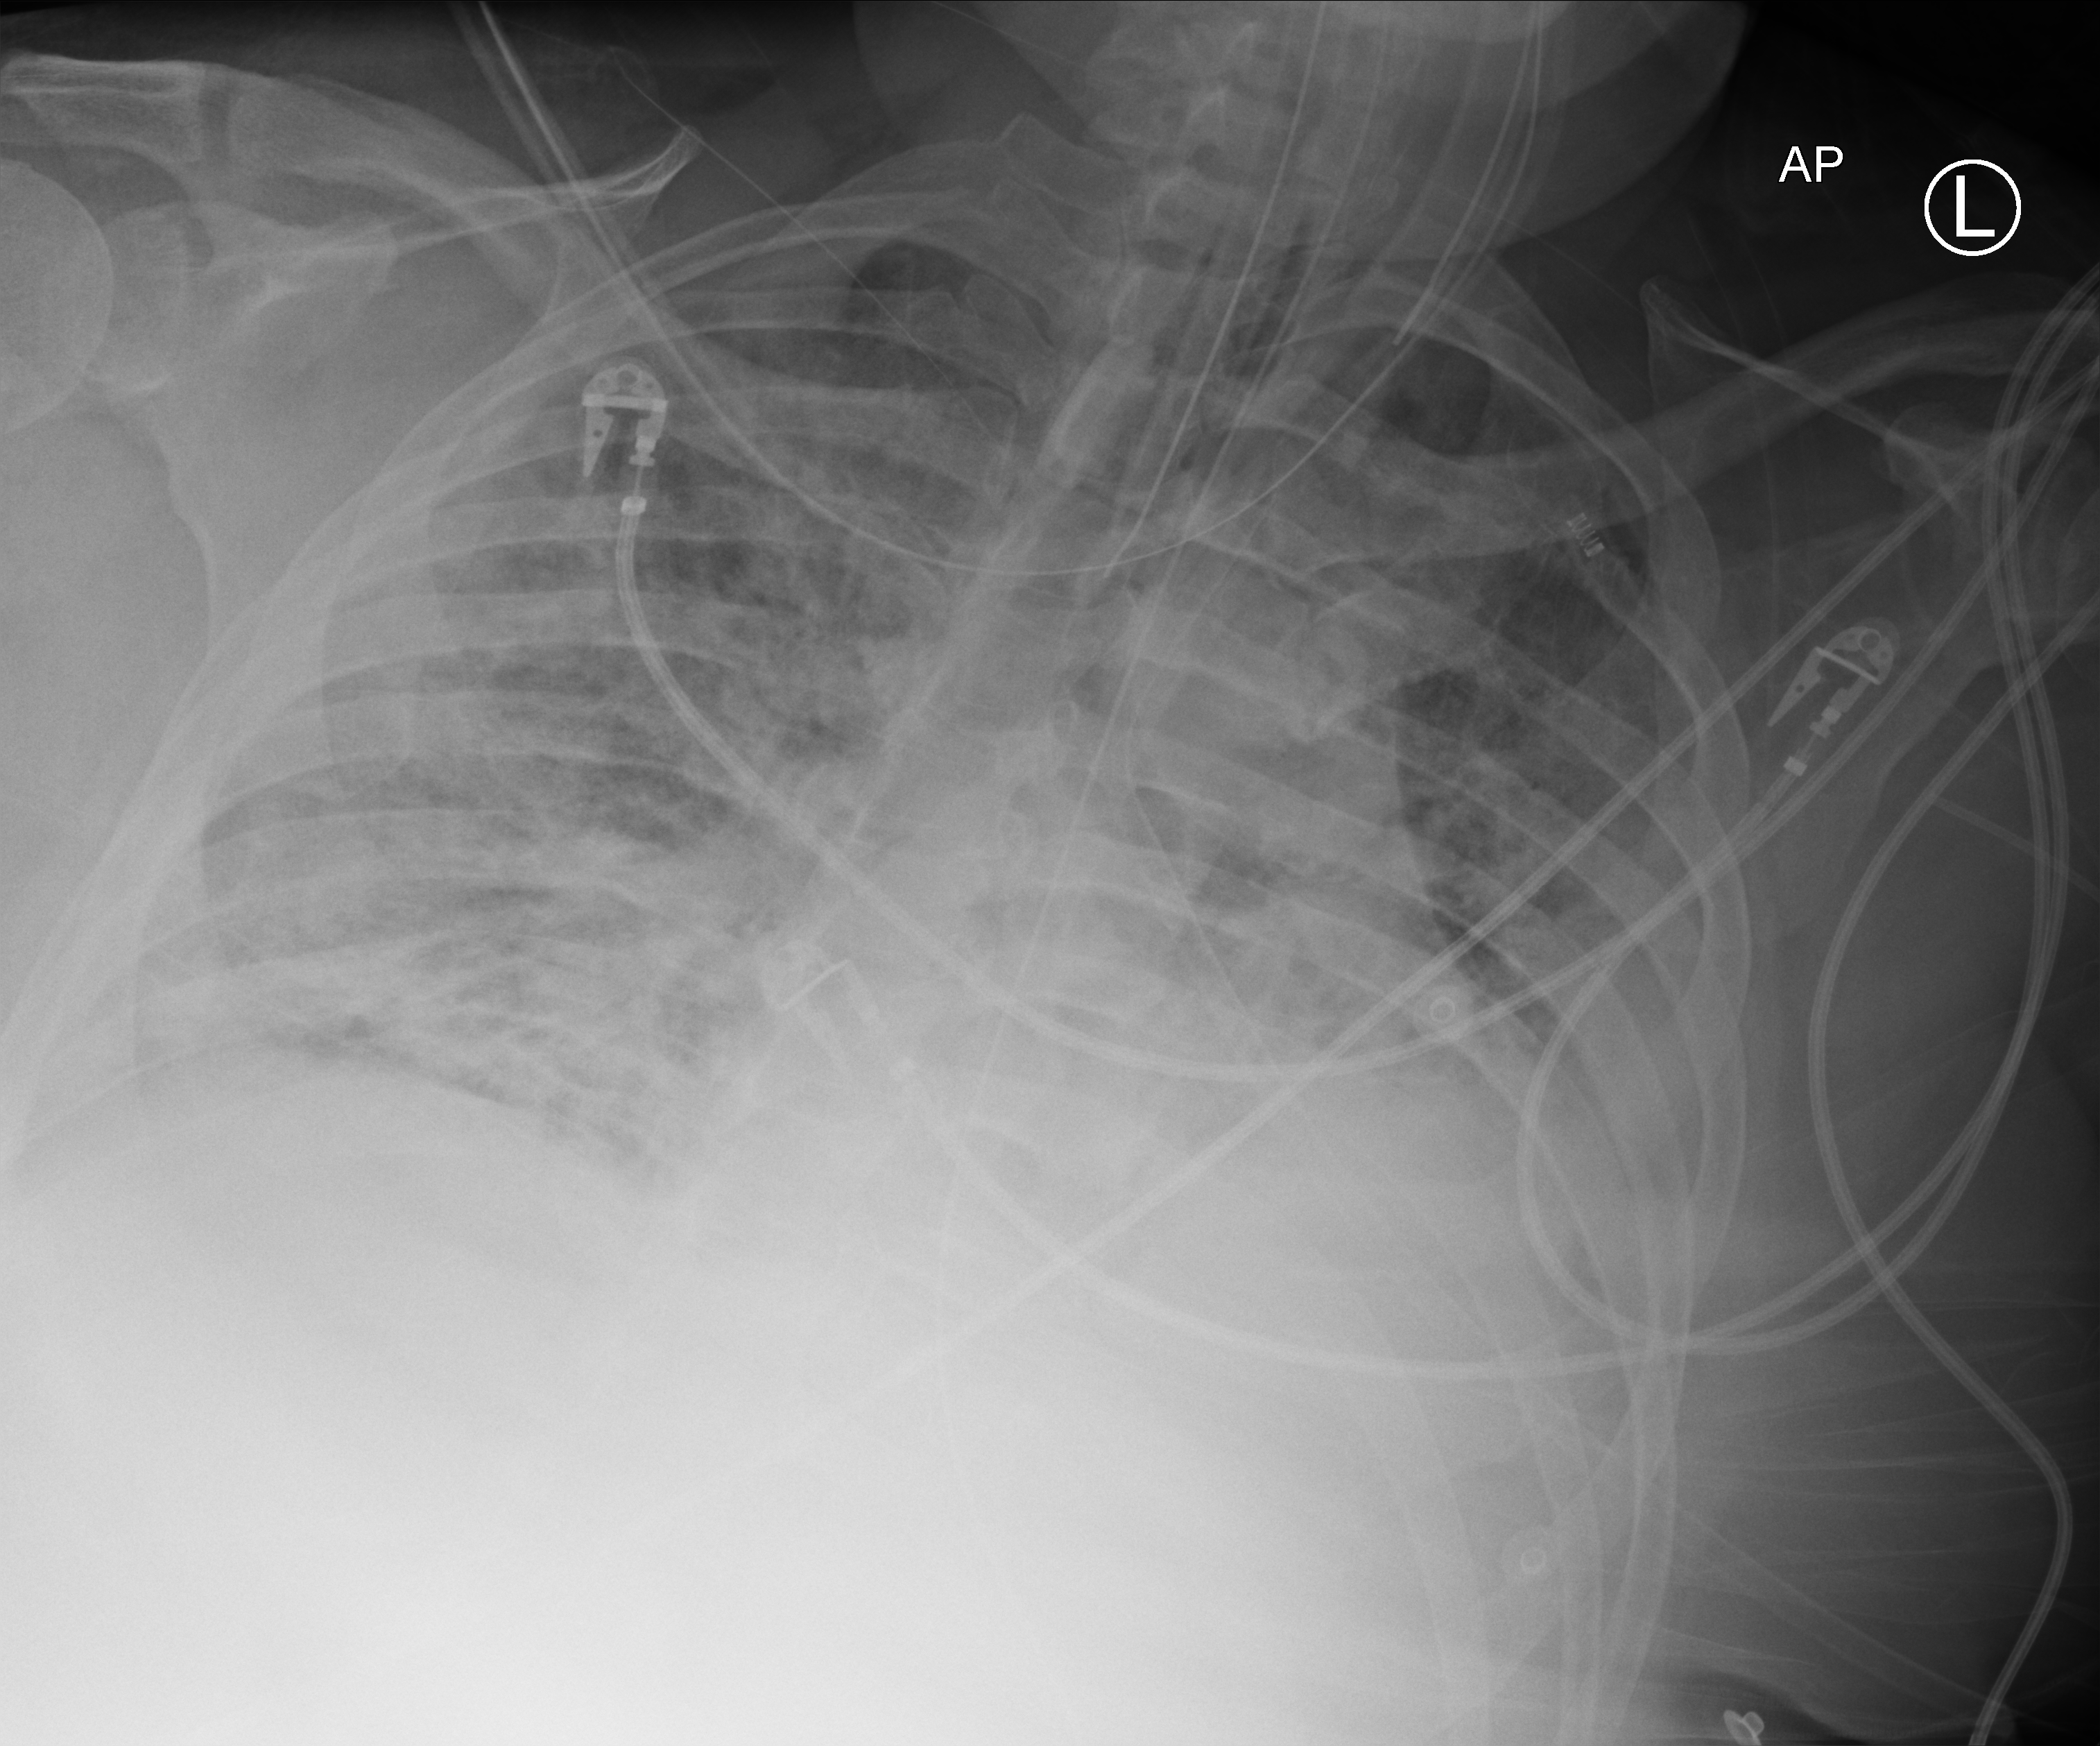
Chest X-ray (portable), anteroposterior (AP) projection. Male patient hospitalised with COVID-19, age 18–59 years.
Admission-level facts for this patient (not findings on this image; timing relative to this image not recorded): hypertension (admission record): yes.